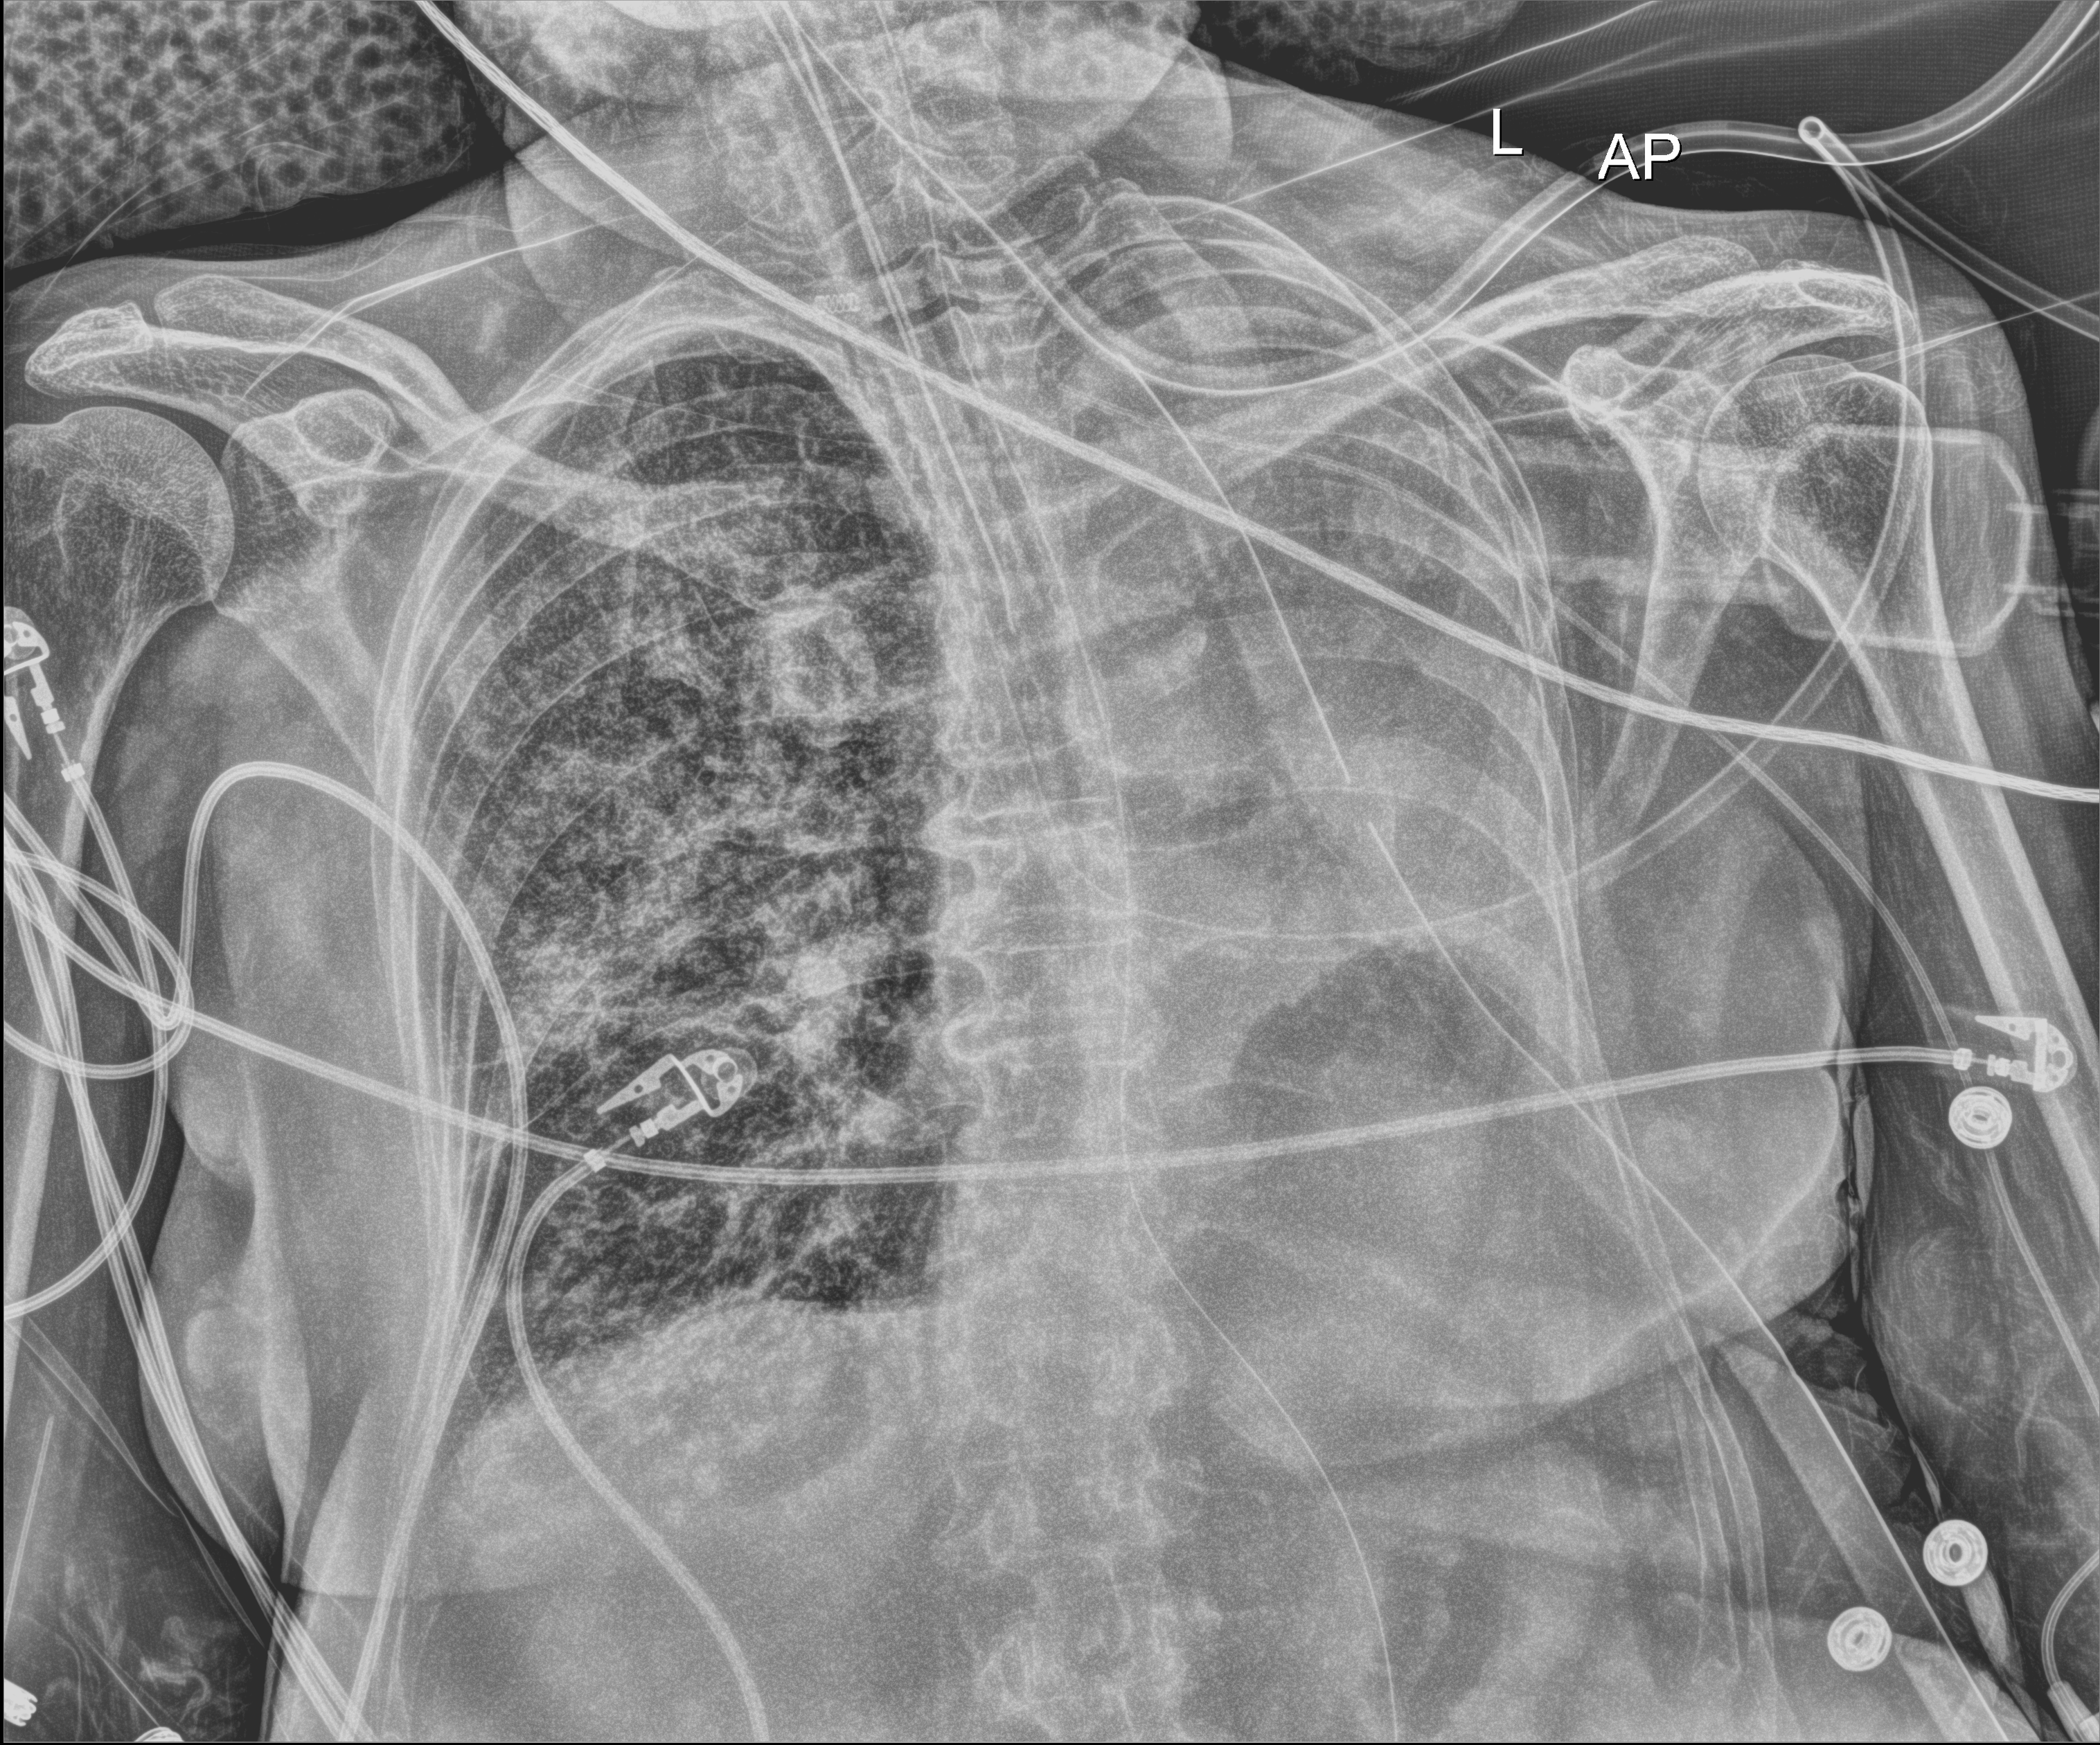
Bedside chest radiograph (digital radiography); anteroposterior (AP) projection. Patient hospitalised with COVID-19; female, aged 75–90 years.
From the hospital-stay record, not from the radiograph (when in the stay this image was taken is not recorded): admitted to intensive care during this hospital stay: yes.